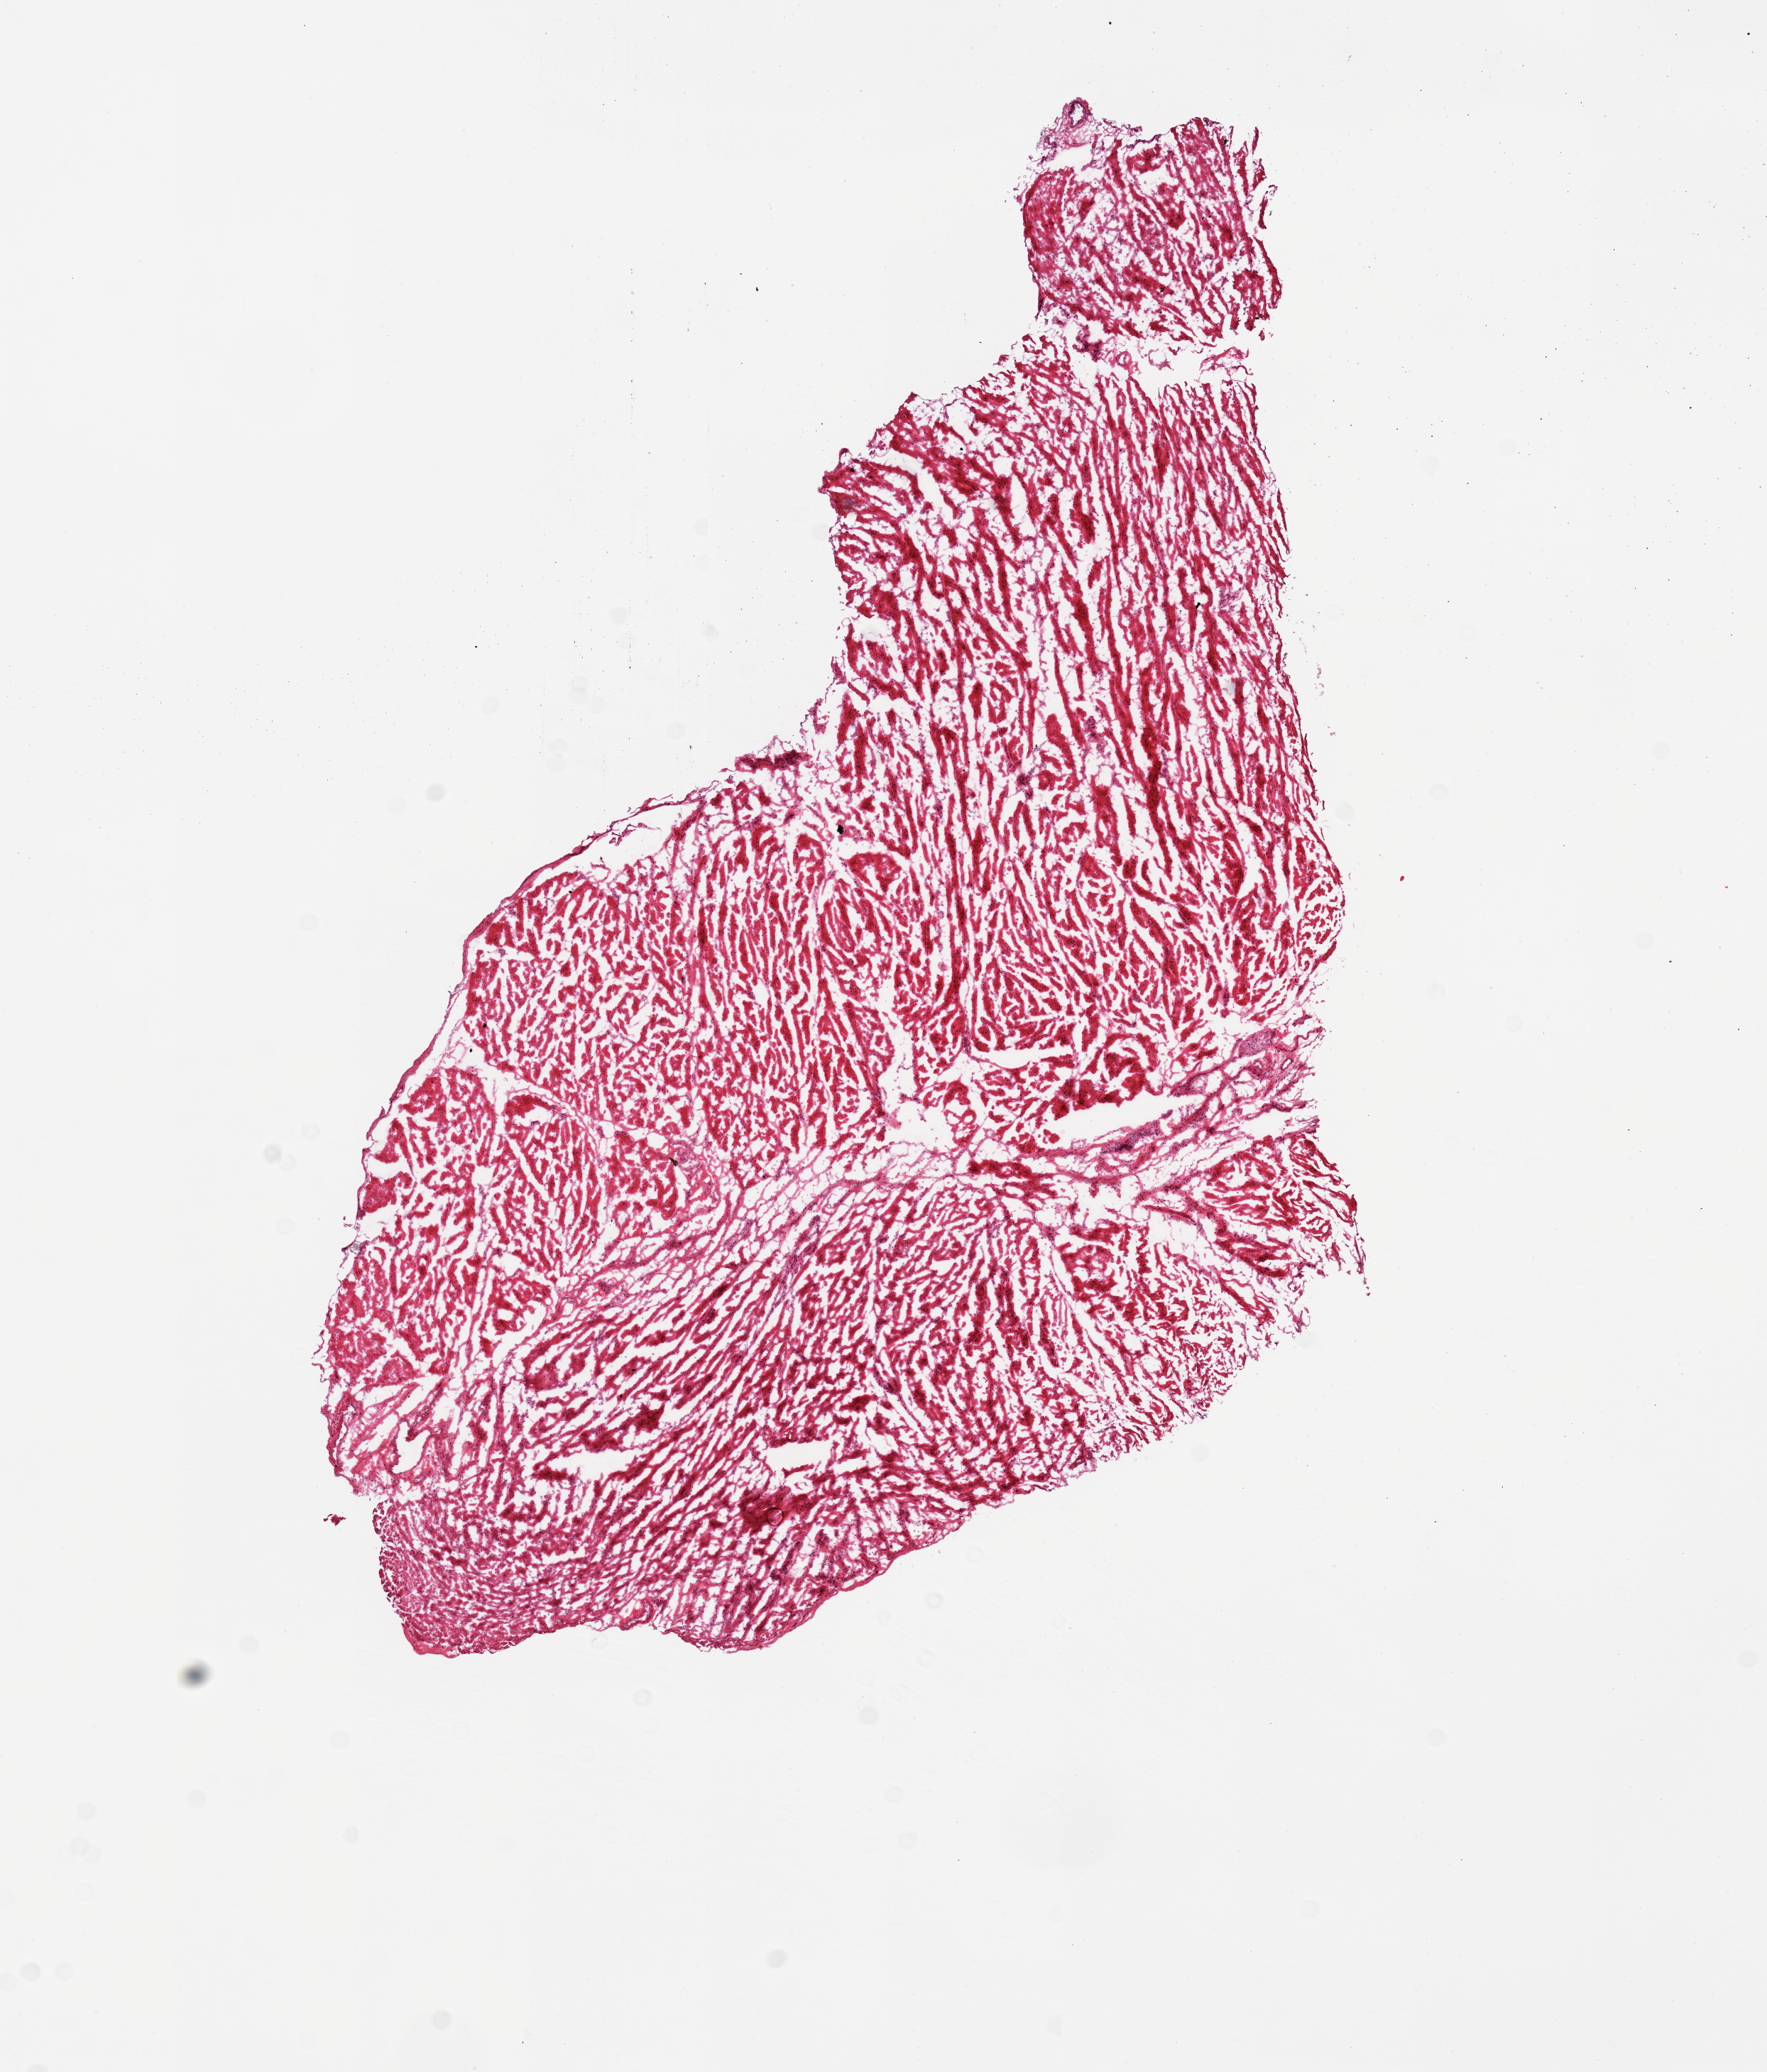
Digitized hematoxylin and eosin (H&E)-stained section, brightfield, whole scanned area (about 9.8 x 11.5 mm, acquisition: 20x scan) shown as a low-resolution overview; frozen section (dry ice); sampled site (target tissue): esophageal muscle; tissue donor sample. Donor sex: female.
• review note (as recorded): 1 piece